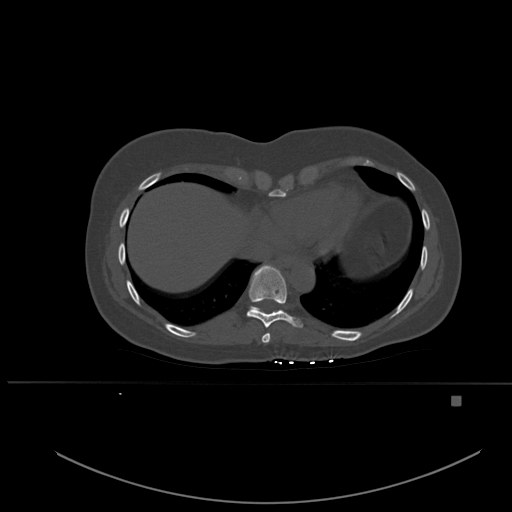
CT including the spine, one axial slice. Slice 304 of 651 in the series (ordered by position). Bone window (W 1800 / L 400 HU). 1.5 mm slice thickness. 512 × 512 image matrix, field of view 443 × 443 mm. Female patient, age 49 years. From the clinical record (not read from this slice): primary cancer: breast.
Annotated regions visible in this slice (semi-automatically segmented with operator editing):
- T10 vertebra: box from (x=251, y=306) to (x=259, y=309) px
- T8 vertebra: (x=261, y=333)–(x=270, y=343)
- T9 vertebra: (x=247, y=265)–(x=303, y=328)